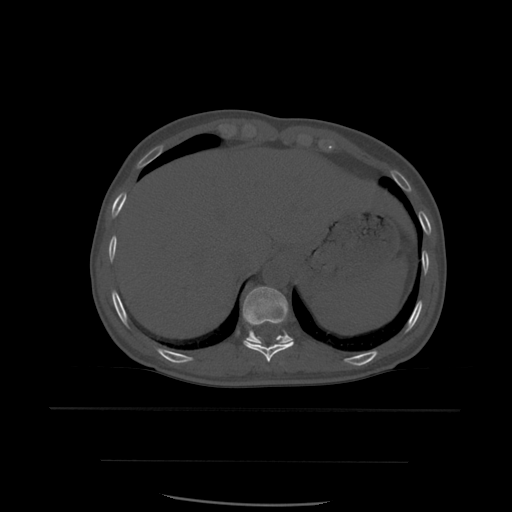
CT including the spine, one axial slice. Slice 308 of 574 in the series (ordered by position). Bone window (W 1800 / L 400 HU). 1.25 mm slice thickness. 512 × 512 image matrix, field of view 392 × 392 mm. Patient age 48 years. From the clinical record (not read from this slice): primary cancer: lung; vertebrae with lytic lesions (as recorded): T11.
Structures marked on this image (semi-automatically segmented with operator editing):
- T10 vertebra: box from (x=244, y=320) to (x=294, y=362) px
- T11 vertebra: (x=243, y=287)–(x=294, y=346)